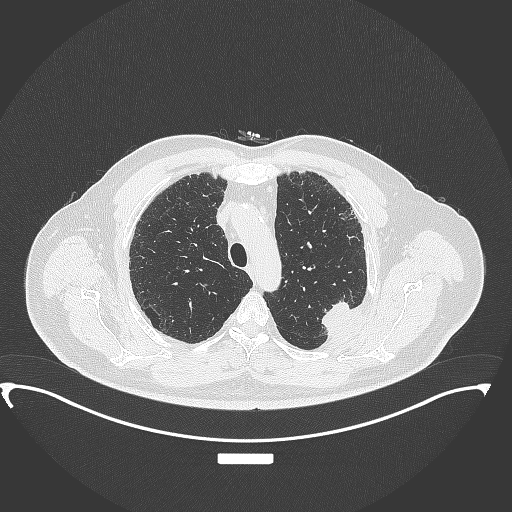
Chest CT, one axial slice; slice 279 of 350 in the series (ordered by position); reconstruction kernel B70f; 120 kVp; lung window (W 1500 / L -600 HU); 1 mm slice thickness; 512 × 512 image matrix, field of view 459 × 459 mm. Patient: male, 64 years. Case-level facts recorded for this patient, not image findings: clinical TNM (as recorded): T1c N1 M1.
Annotated regions visible in this slice (bounding box drawn by a radiologist):
- lung tumour (recorded histology: adenocarcinoma): bounding box (x1, y1, x2, y2) in pixels: (315, 297, 359, 345)